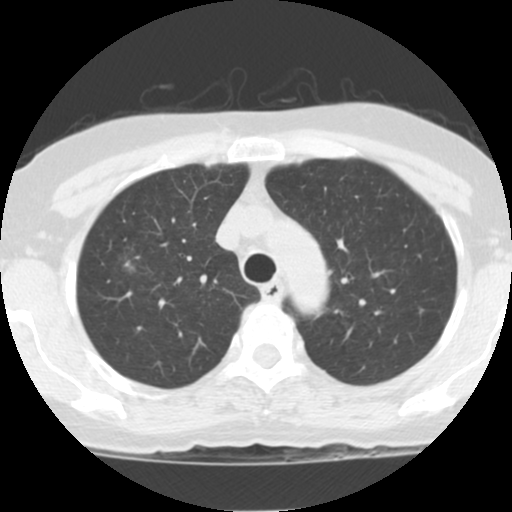
Chest CT (low-dose screening protocol), one axial image; second annual screen; lung window (W 1500 / L -600 HU); slice 26 of 118 in the series. Female participant, aged 62 years at enrolment. Current smoker at enrolment.
Expert-annotated lung lesion, box from (x=108, y=245) to (x=151, y=289) px. The exam's reader record, not a measurement of the box and not confirmed to be the same lesion: non-calcified nodule or mass ≥4 mm, right upper lobe, 8 × 7 mm, poorly defined margins, ground glass attenuation, pre-existing on the prior screen: yes; interval growth: yes. Official screen result: positive, other.